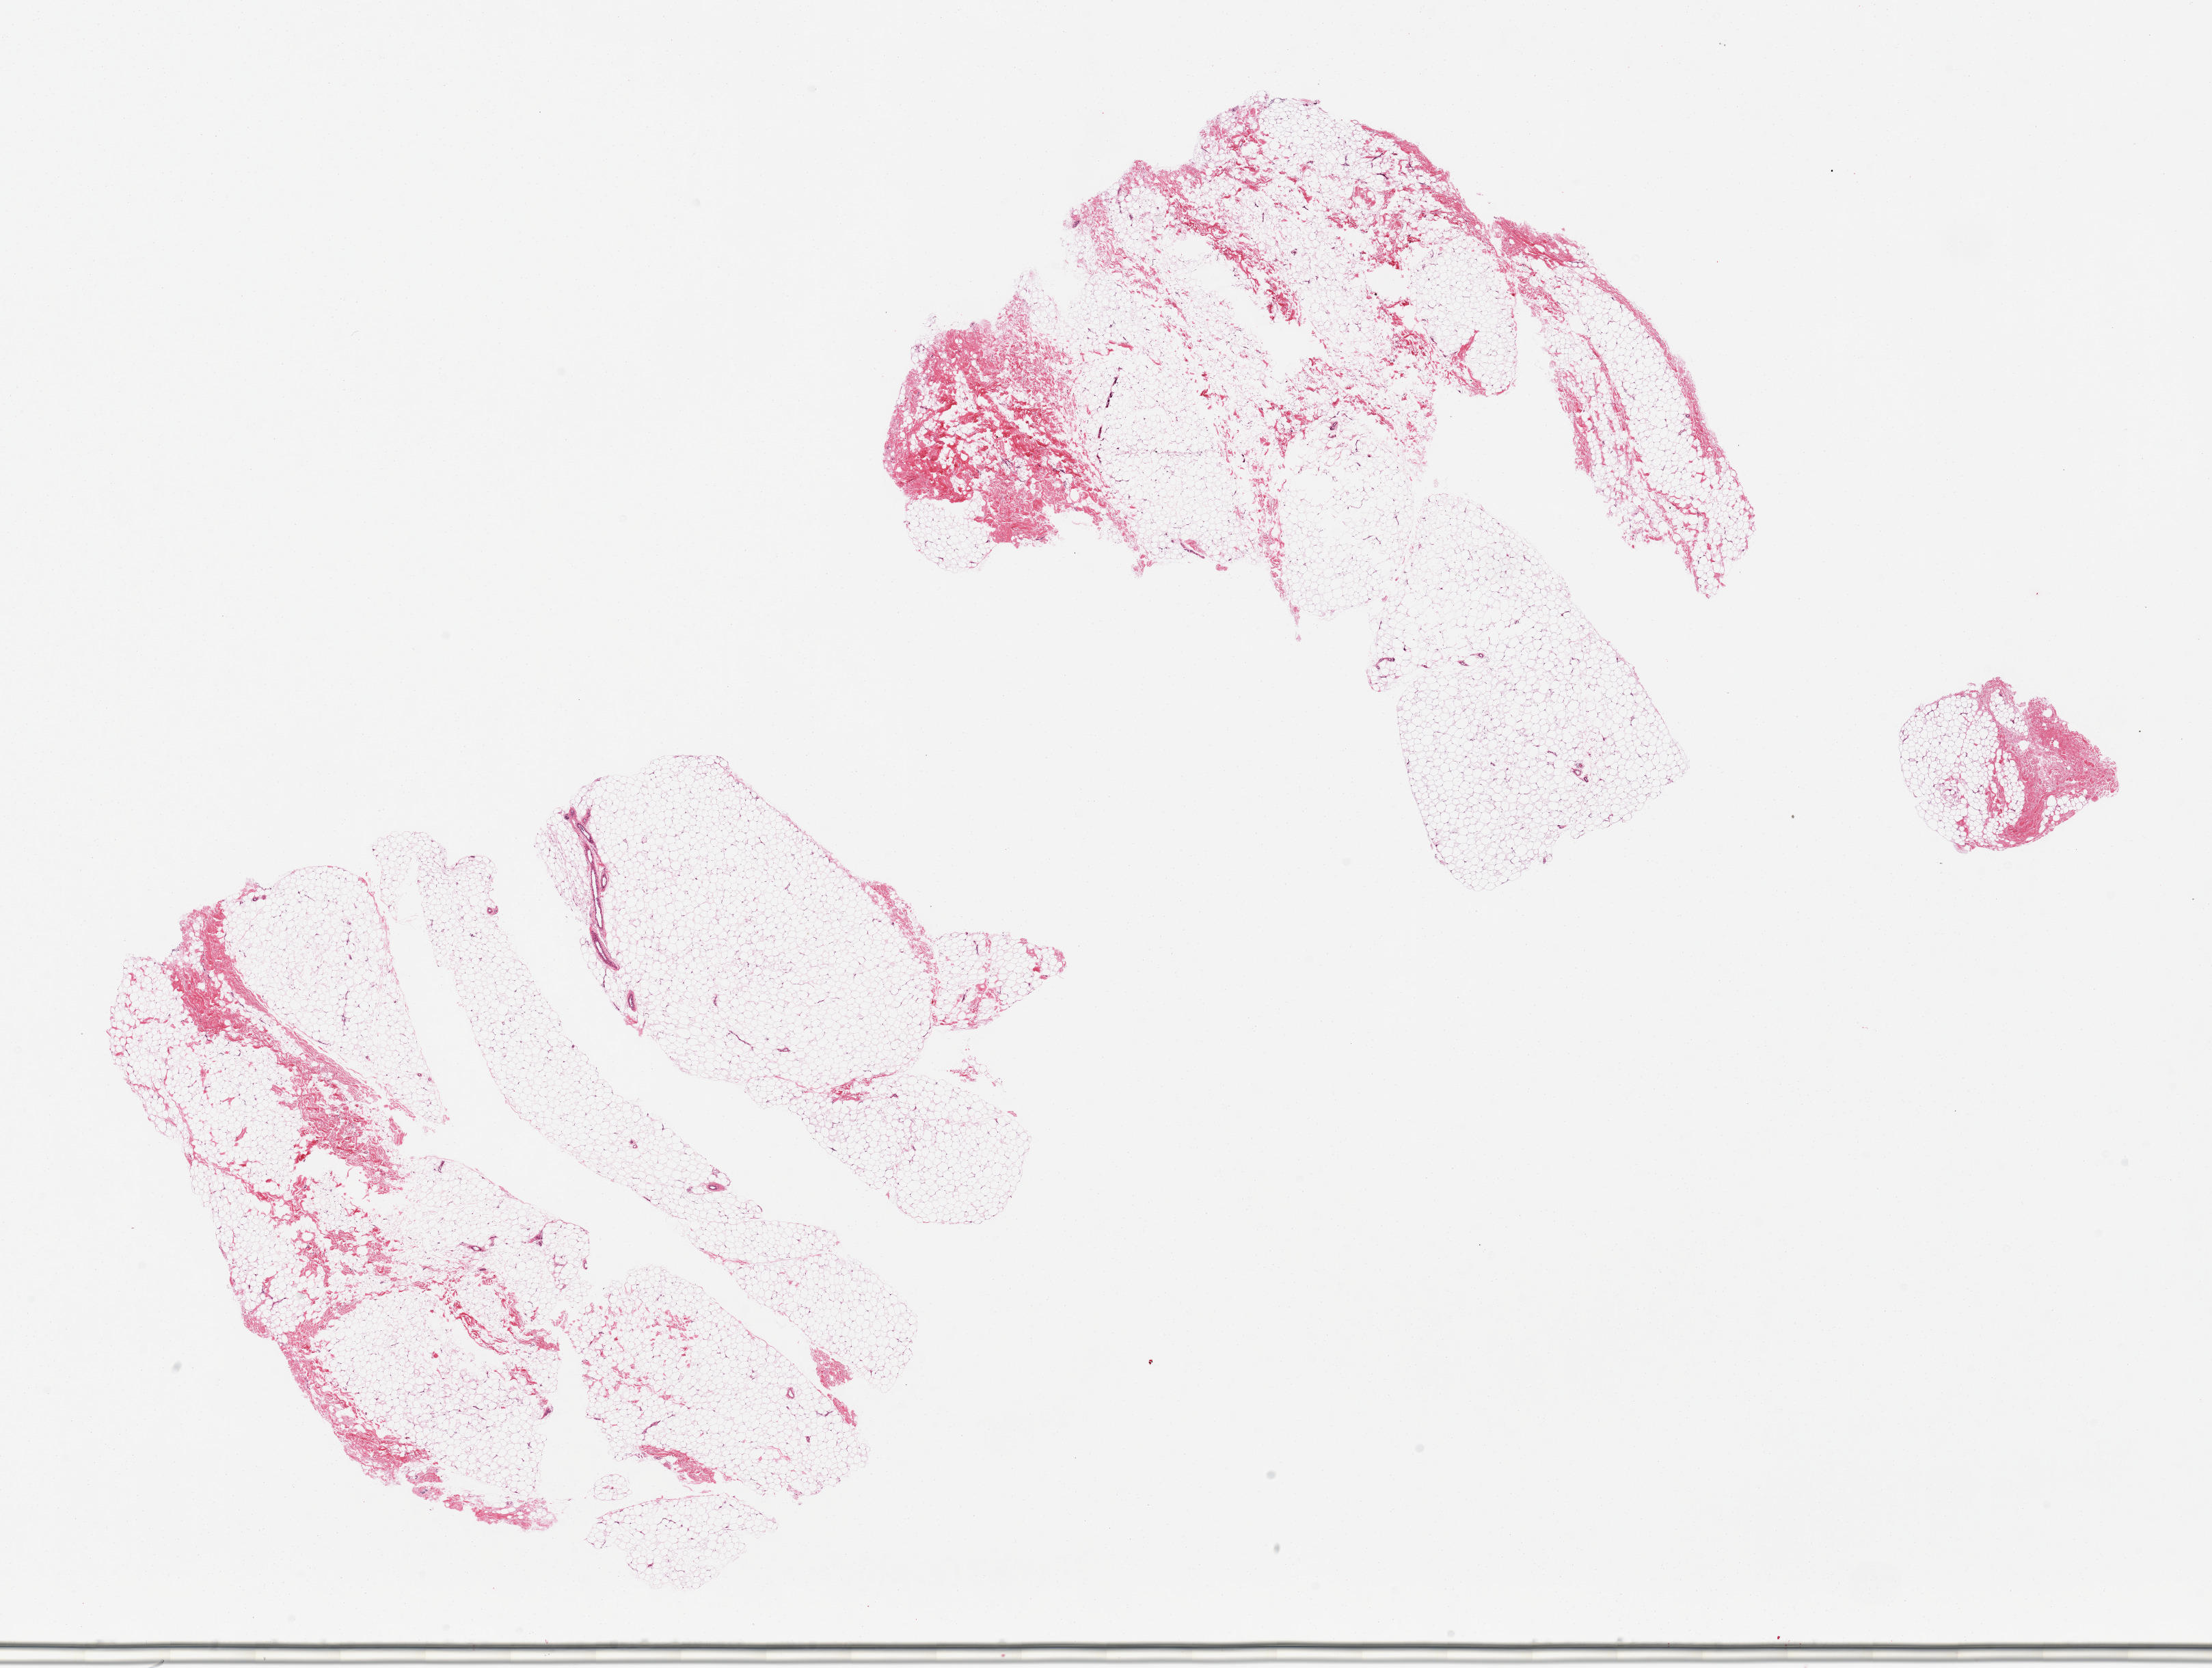
H&E whole-slide image, low-resolution overview of the scanned area, about 25.6 x 19.3 mm, PAXgene-fixed paraffin-embedded (PFPE) section, section of breast (target tissue), donor tissue sample. Donor sex: male.
Pathologist's review note for this sample: 2 pieces, fibroadipose tissue, no ductal elements noted.